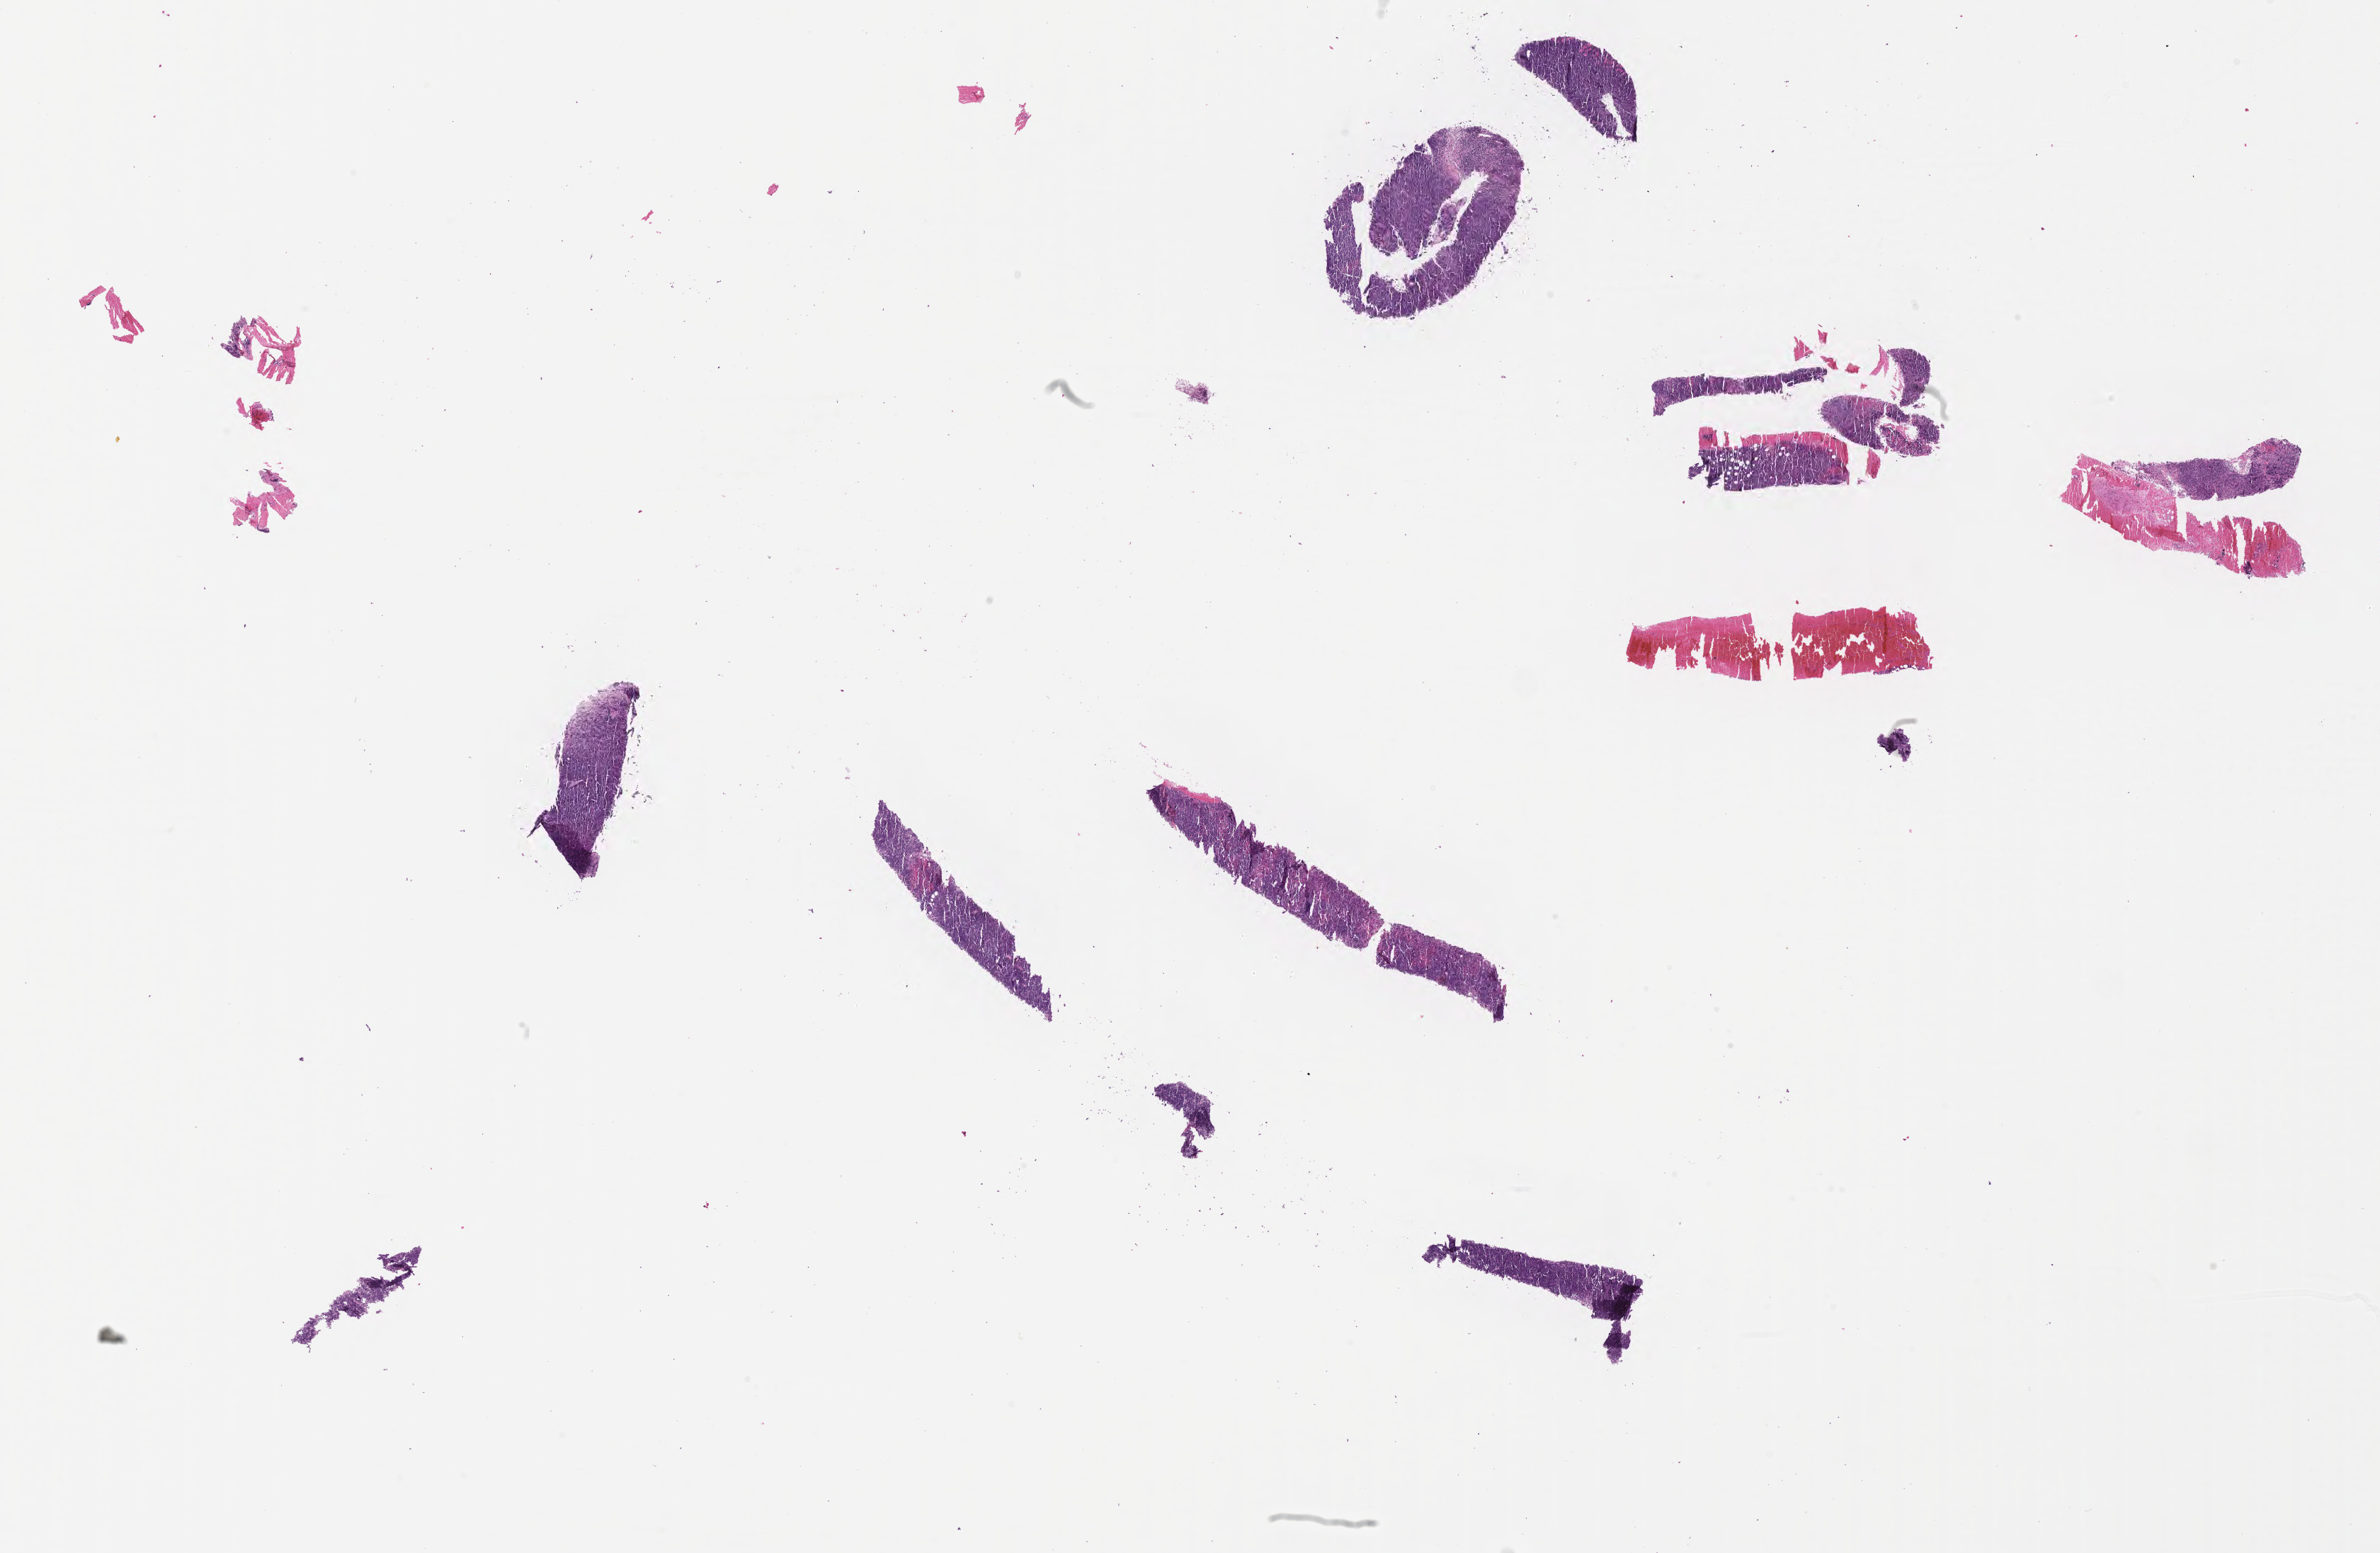
Digitized haematoxylin and eosin-stained section, a low-resolution overview of the entire scanned area, about 27.2 x 17.7 mm; formalin-fixed, paraffin-embedded (FFPE) tissue; primary tumor. Patient: male, 45 years old. Slide review estimates, as recorded: tumor cells 70%, tumor nuclei 90%, stromal cells 10%, necrosis 20%, normal cells 0%. Inflammatory infiltration, as recorded: lymphocyte infiltration 50%, monocyte infiltration 20%, neutrophil infiltration 5%.
Section: top of the tissue portion. Ann Arbor stage (patient): Stage IV. Histologic diagnosis: Burkitt lymphoma, NOS.